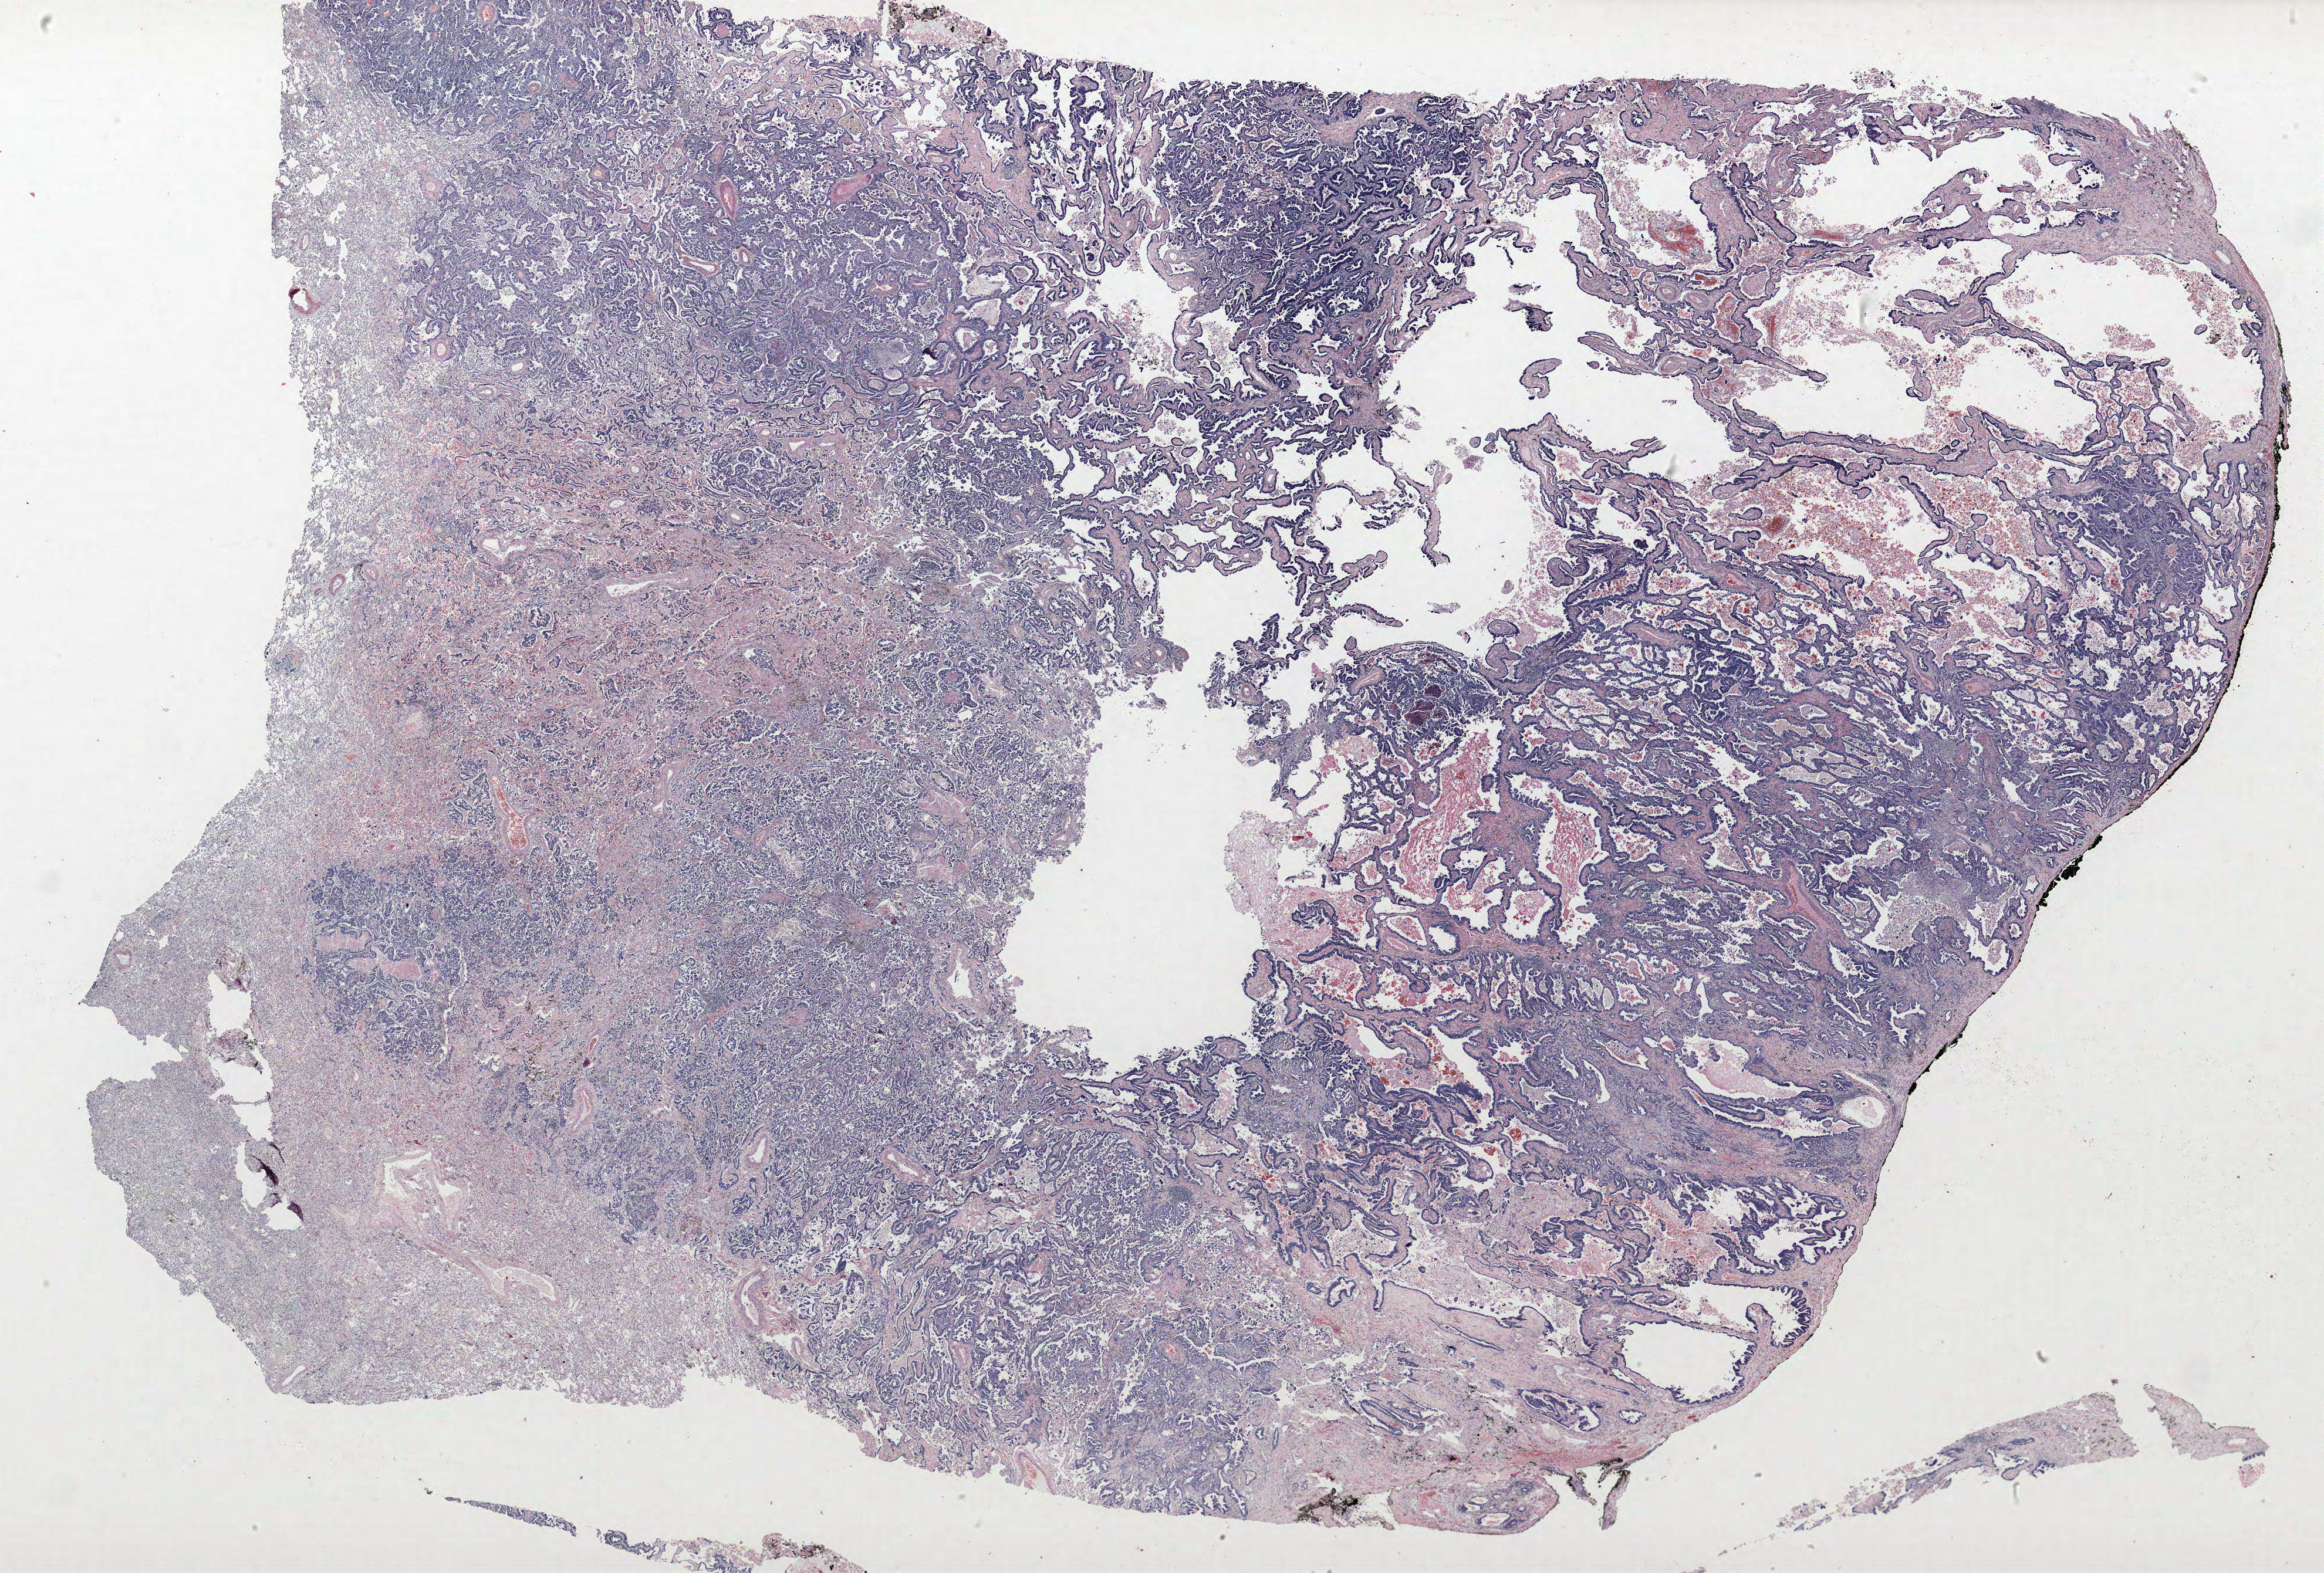
Whole-slide histology image, H&E-stained, low-resolution overview of the scanned area, about 31.7 x 21.5 mm. FFPE section. Lung. Male patient, aged 55 at enrolment. Current smoker at enrolment. Grade: moderately differentiated (G2).
Primary tumour location (clinical record): right lower lobe. Participant's lung-cancer diagnosis: Adenocarcinoma, NOS. Stage (AJCC 6th edition): IB. Tumour size (pathology): 75 mm. Note: participant had 2 primary lung cancers recorded; fields above describe the first.